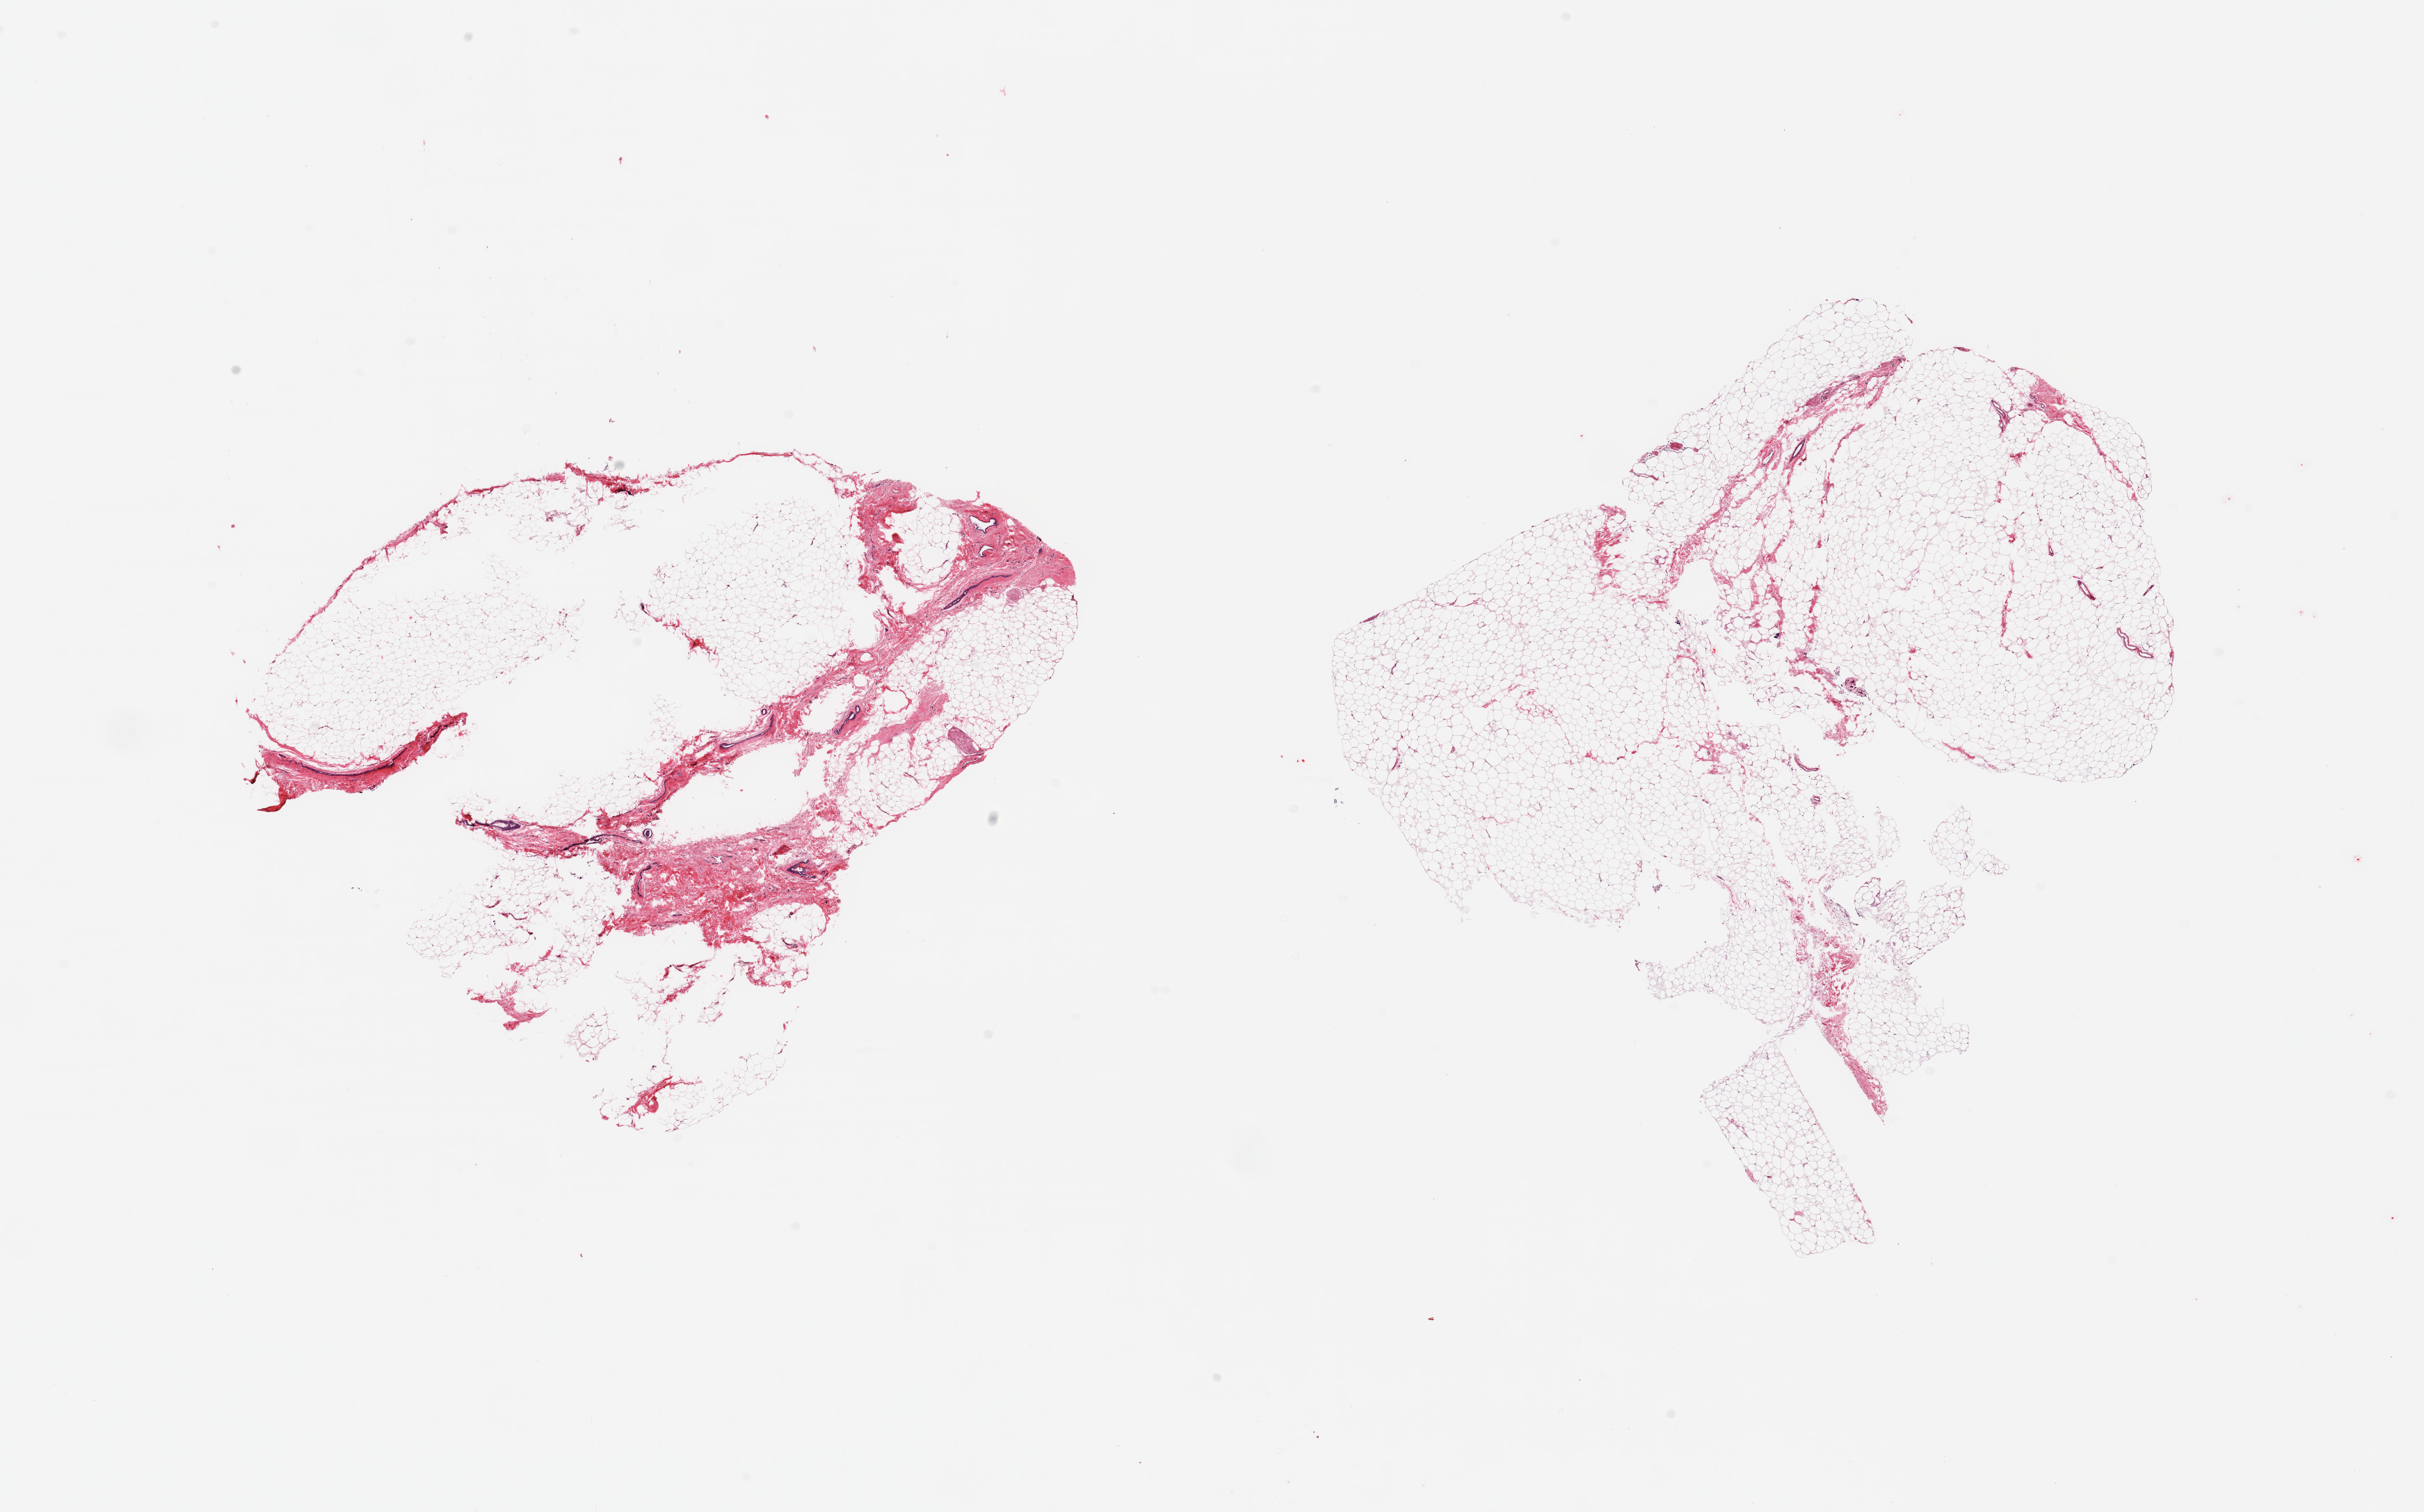
Digitized hematoxylin and eosin (H&E)-stained section — whole scanned area (about 27.6 x 17.2 mm, from a 20x scan) shown as a low-resolution overview, PAXgene-fixed paraffin-embedded (PFPE) section, sampled site (target tissue): breast, tissue donor sample. Donor sex: male.
• pathologist's review note for this sample: 2 pieces; scattered ducts in fibrofatty tissue